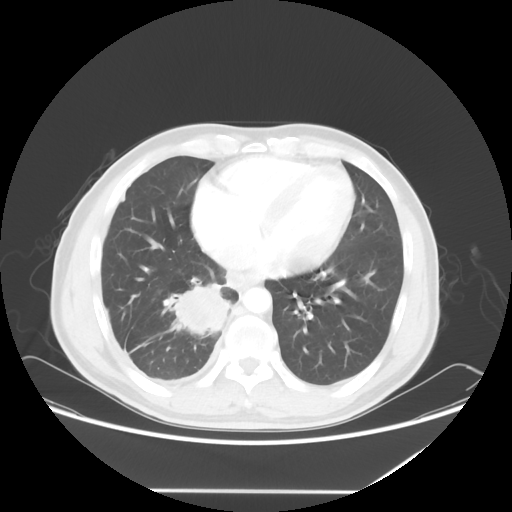
Chest CT, one axial slice; slice 21 of 60 in the series (ordered by position); reconstruction kernel STANDARD; lung window (W 1500 / L -600 HU); 5 mm slice thickness; 512 × 512 image matrix. Patient: male, 48 years. From the clinical record (not read from this slice): clinical TNM (as recorded): T3 N3 M1a.
Structures marked on this image (bounding box drawn by a radiologist):
- lung tumour (recorded histology: squamous cell carcinoma): bounding box <160,280,234,344> (left, top, right, bottom; pixels)